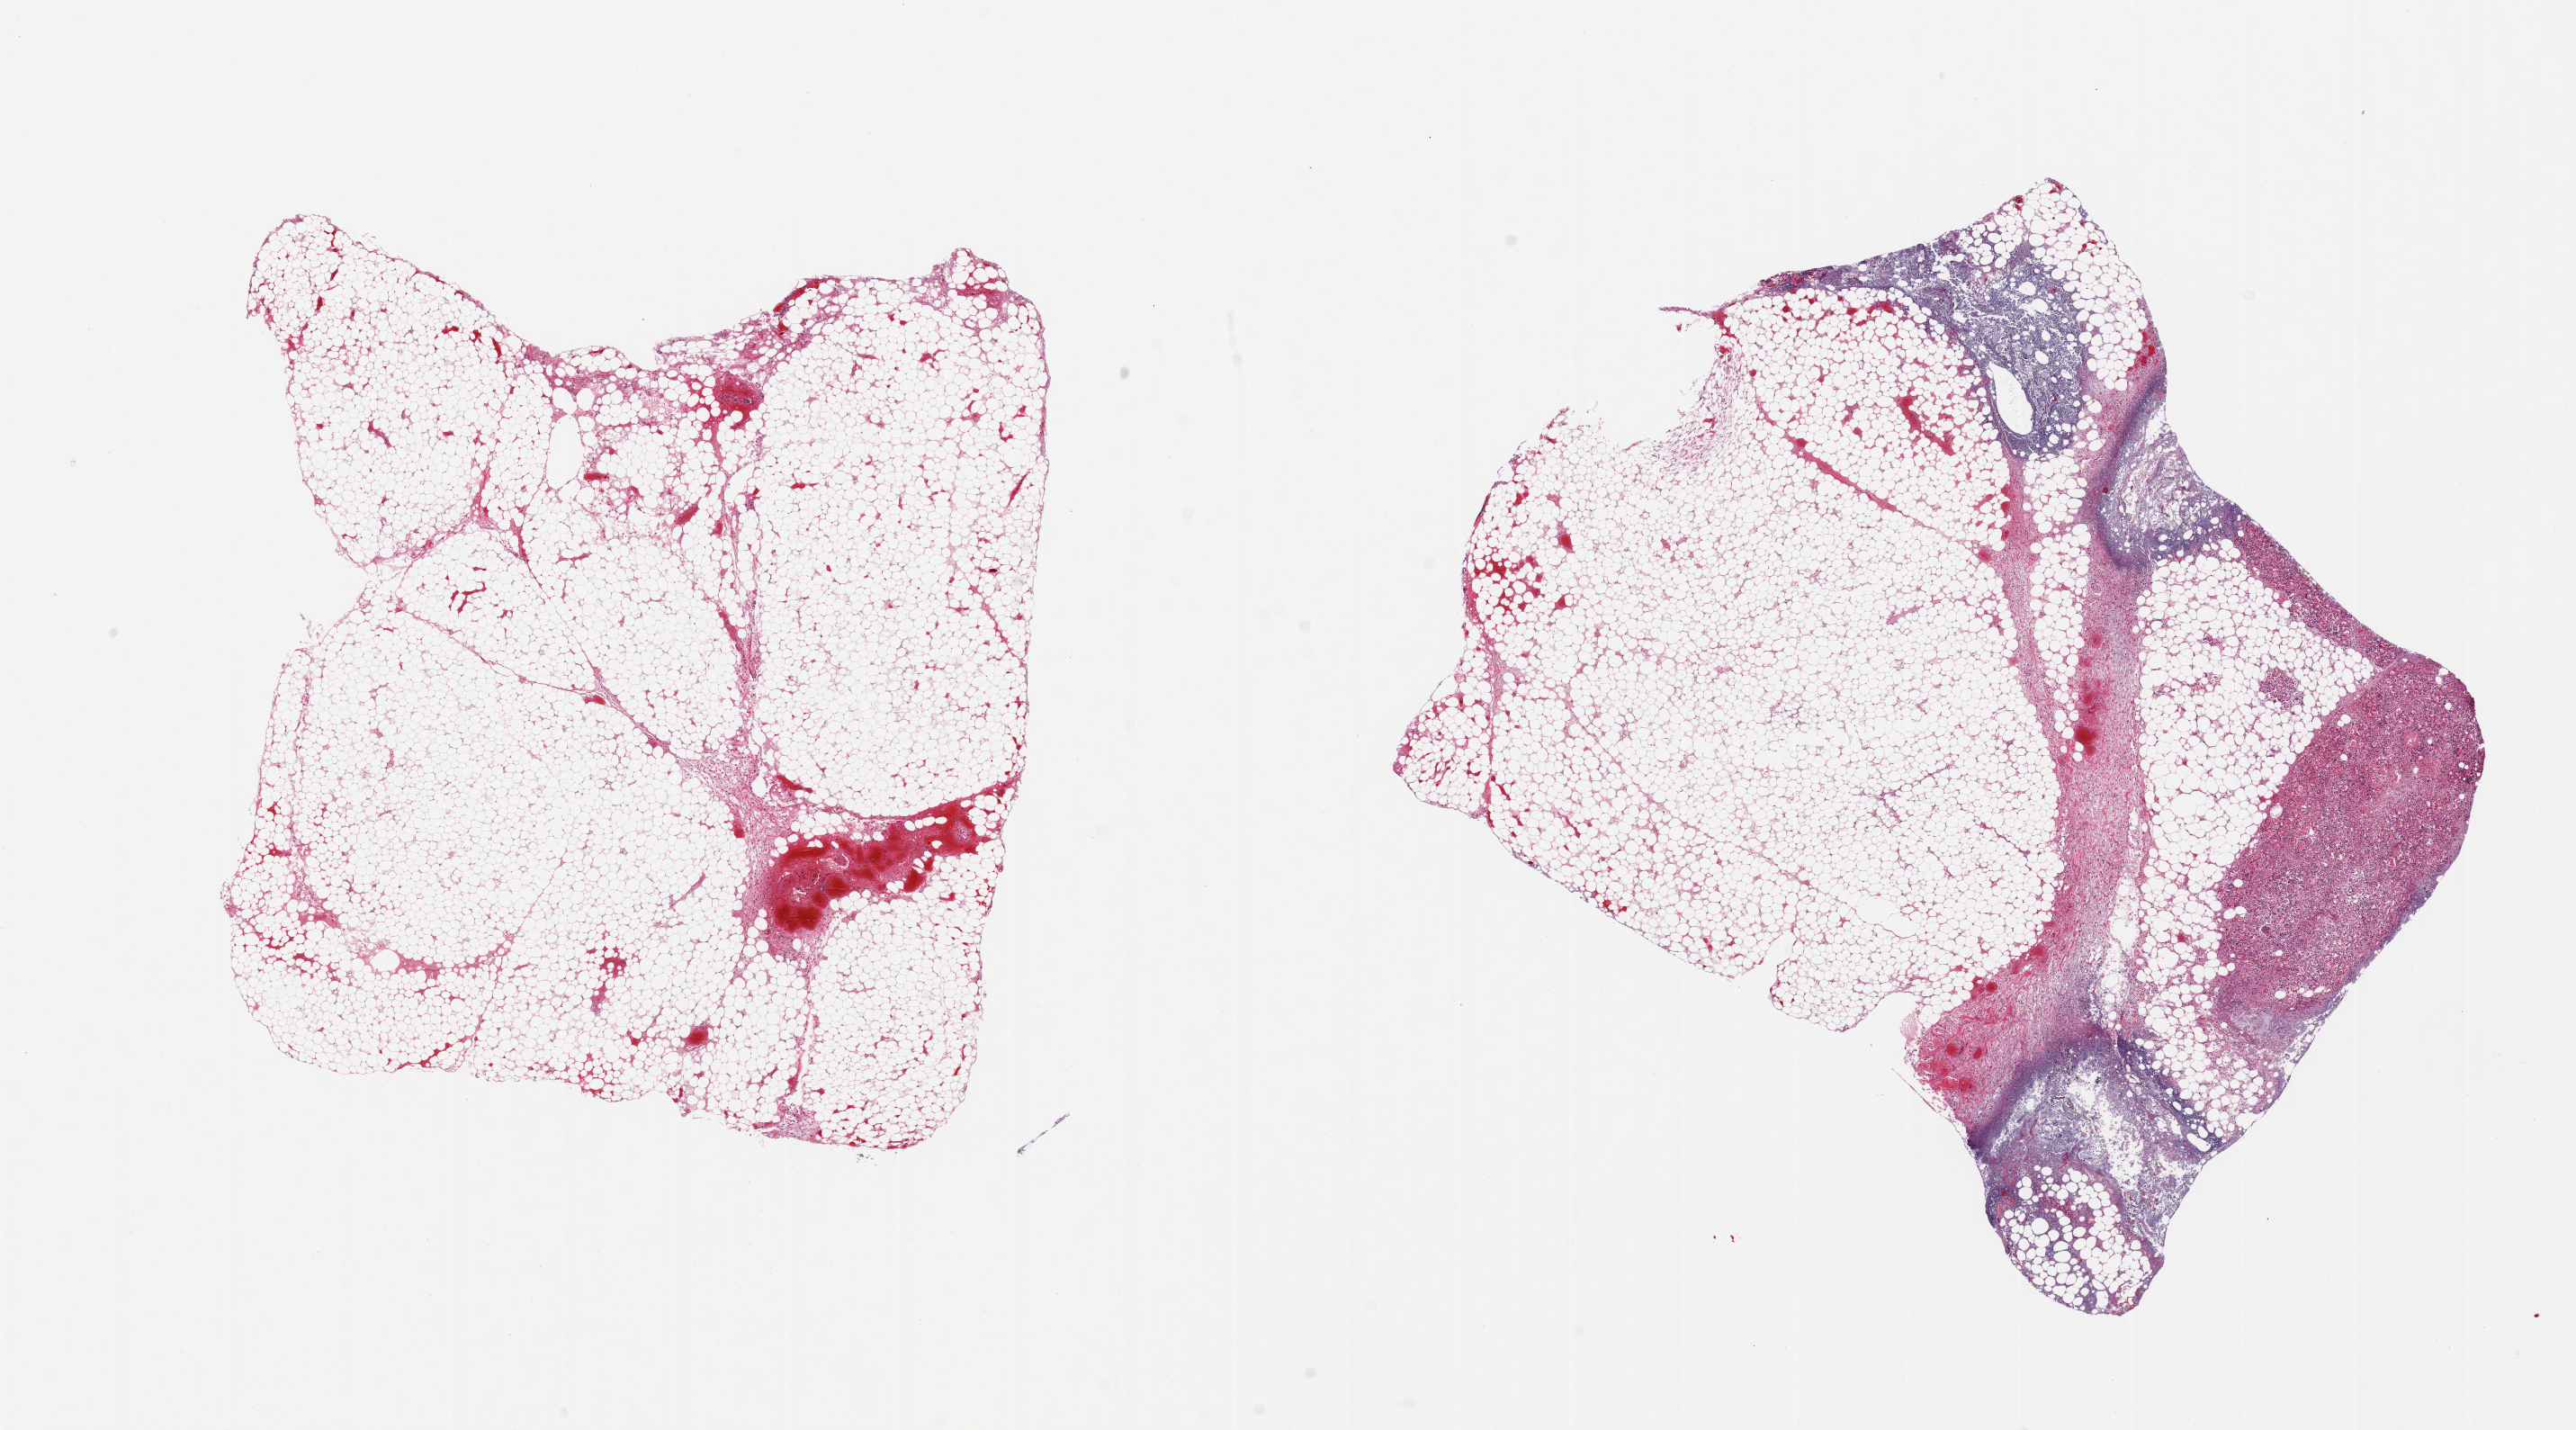
Whole-slide image, H&E stain, brightfield — shown as a low-resolution overview of the whole scanned area (about 22.6 x 12.6 mm, slide scanned at 20x); PAXgene-fixed paraffin-embedded (PFPE) section; sampled site (target tissue): pancreas; tissue donor sample. Donor sex: male.
* pathologist's review note for this sample: 2 pieces, 90% badly autolyzed/saponified fat. Small amount of necrotic probable parenchyma